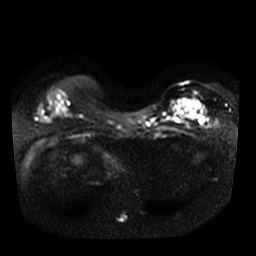
Breast MRI, one axial slice; slice 20 of 36 in the series (ordered by position); diffusion-weighted series; image 2 of 4 stored at this slice position (different b-values; order by instance number); 3 T; 5 mm slice thickness; 256 × 256 image matrix, field of view 320 × 320 mm. Female patient.
Annotated regions visible in this slice (manually delineated by an expert):
- tumour on diffusion-weighted imaging: bounding box [x1, y1, x2, y2] px = [191, 101, 200, 106]